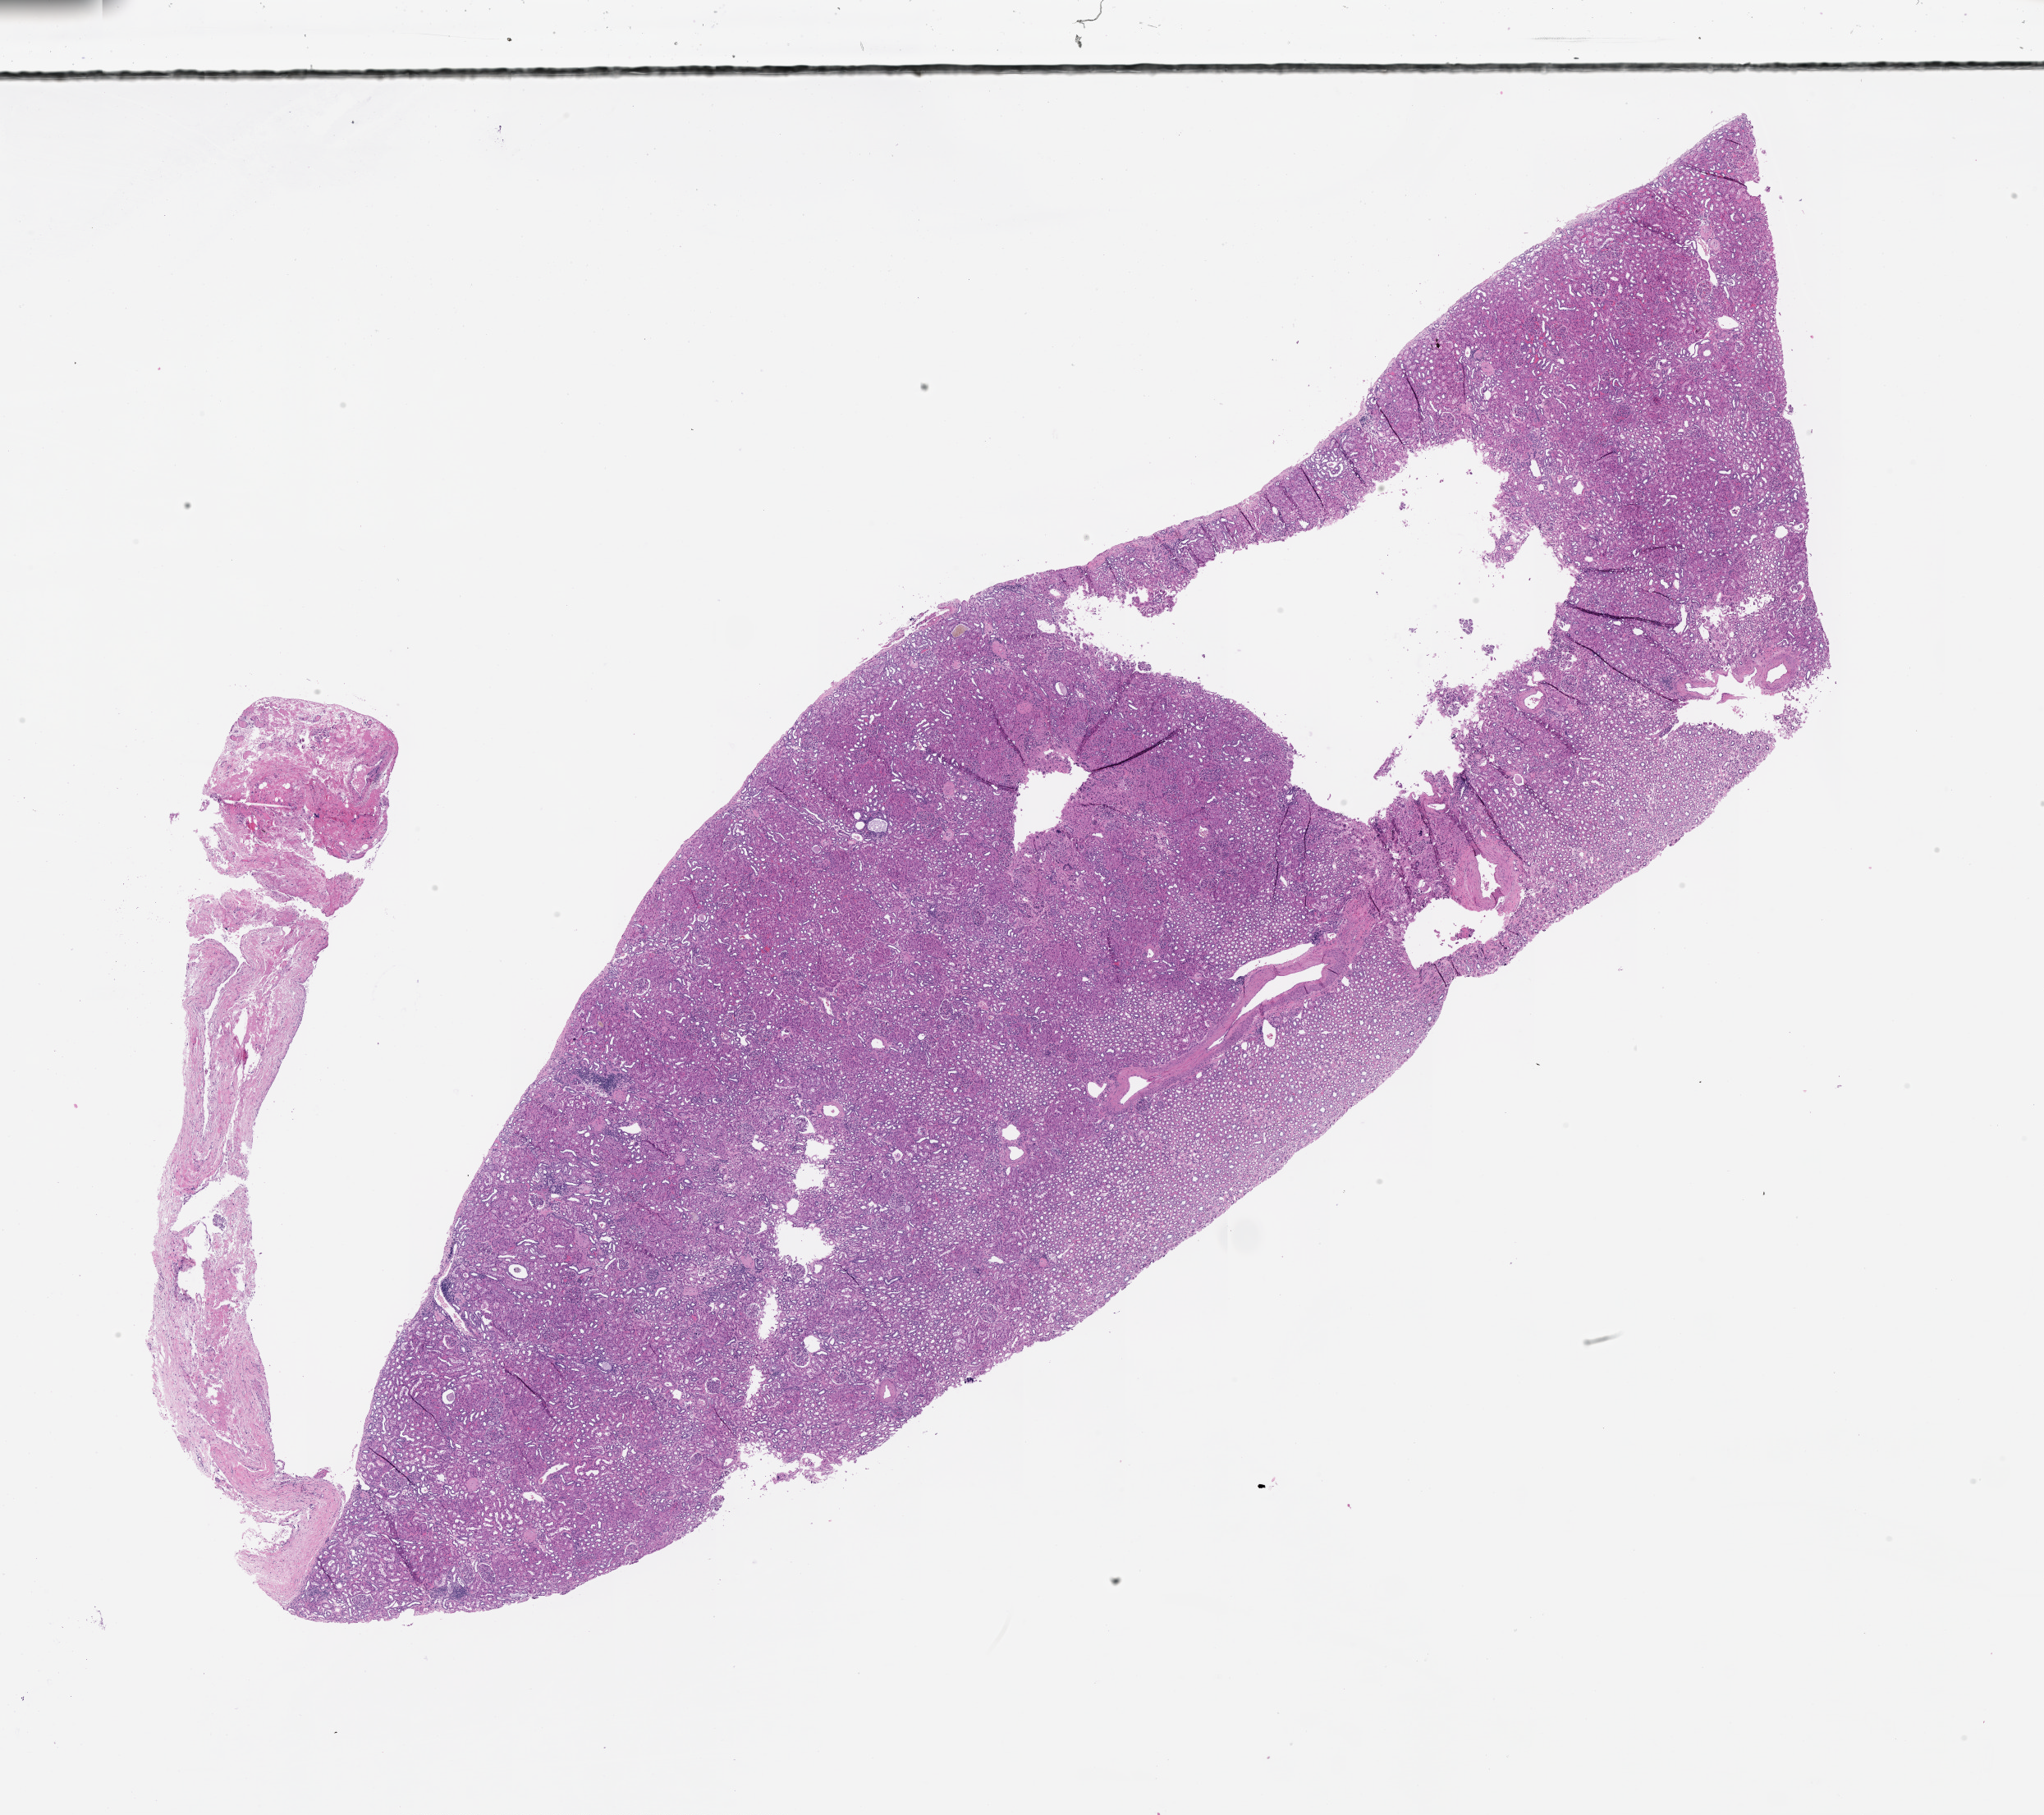
Whole-slide histology image, Hematoxylin and eosin (H&E) stained, a low-resolution overview of the entire scanned area, about 20.0 x 17.8 mm (acquisition: 20x scan).
Patient diagnosis (cohort enrolment): sarcoma (site not recorded at cohort level).